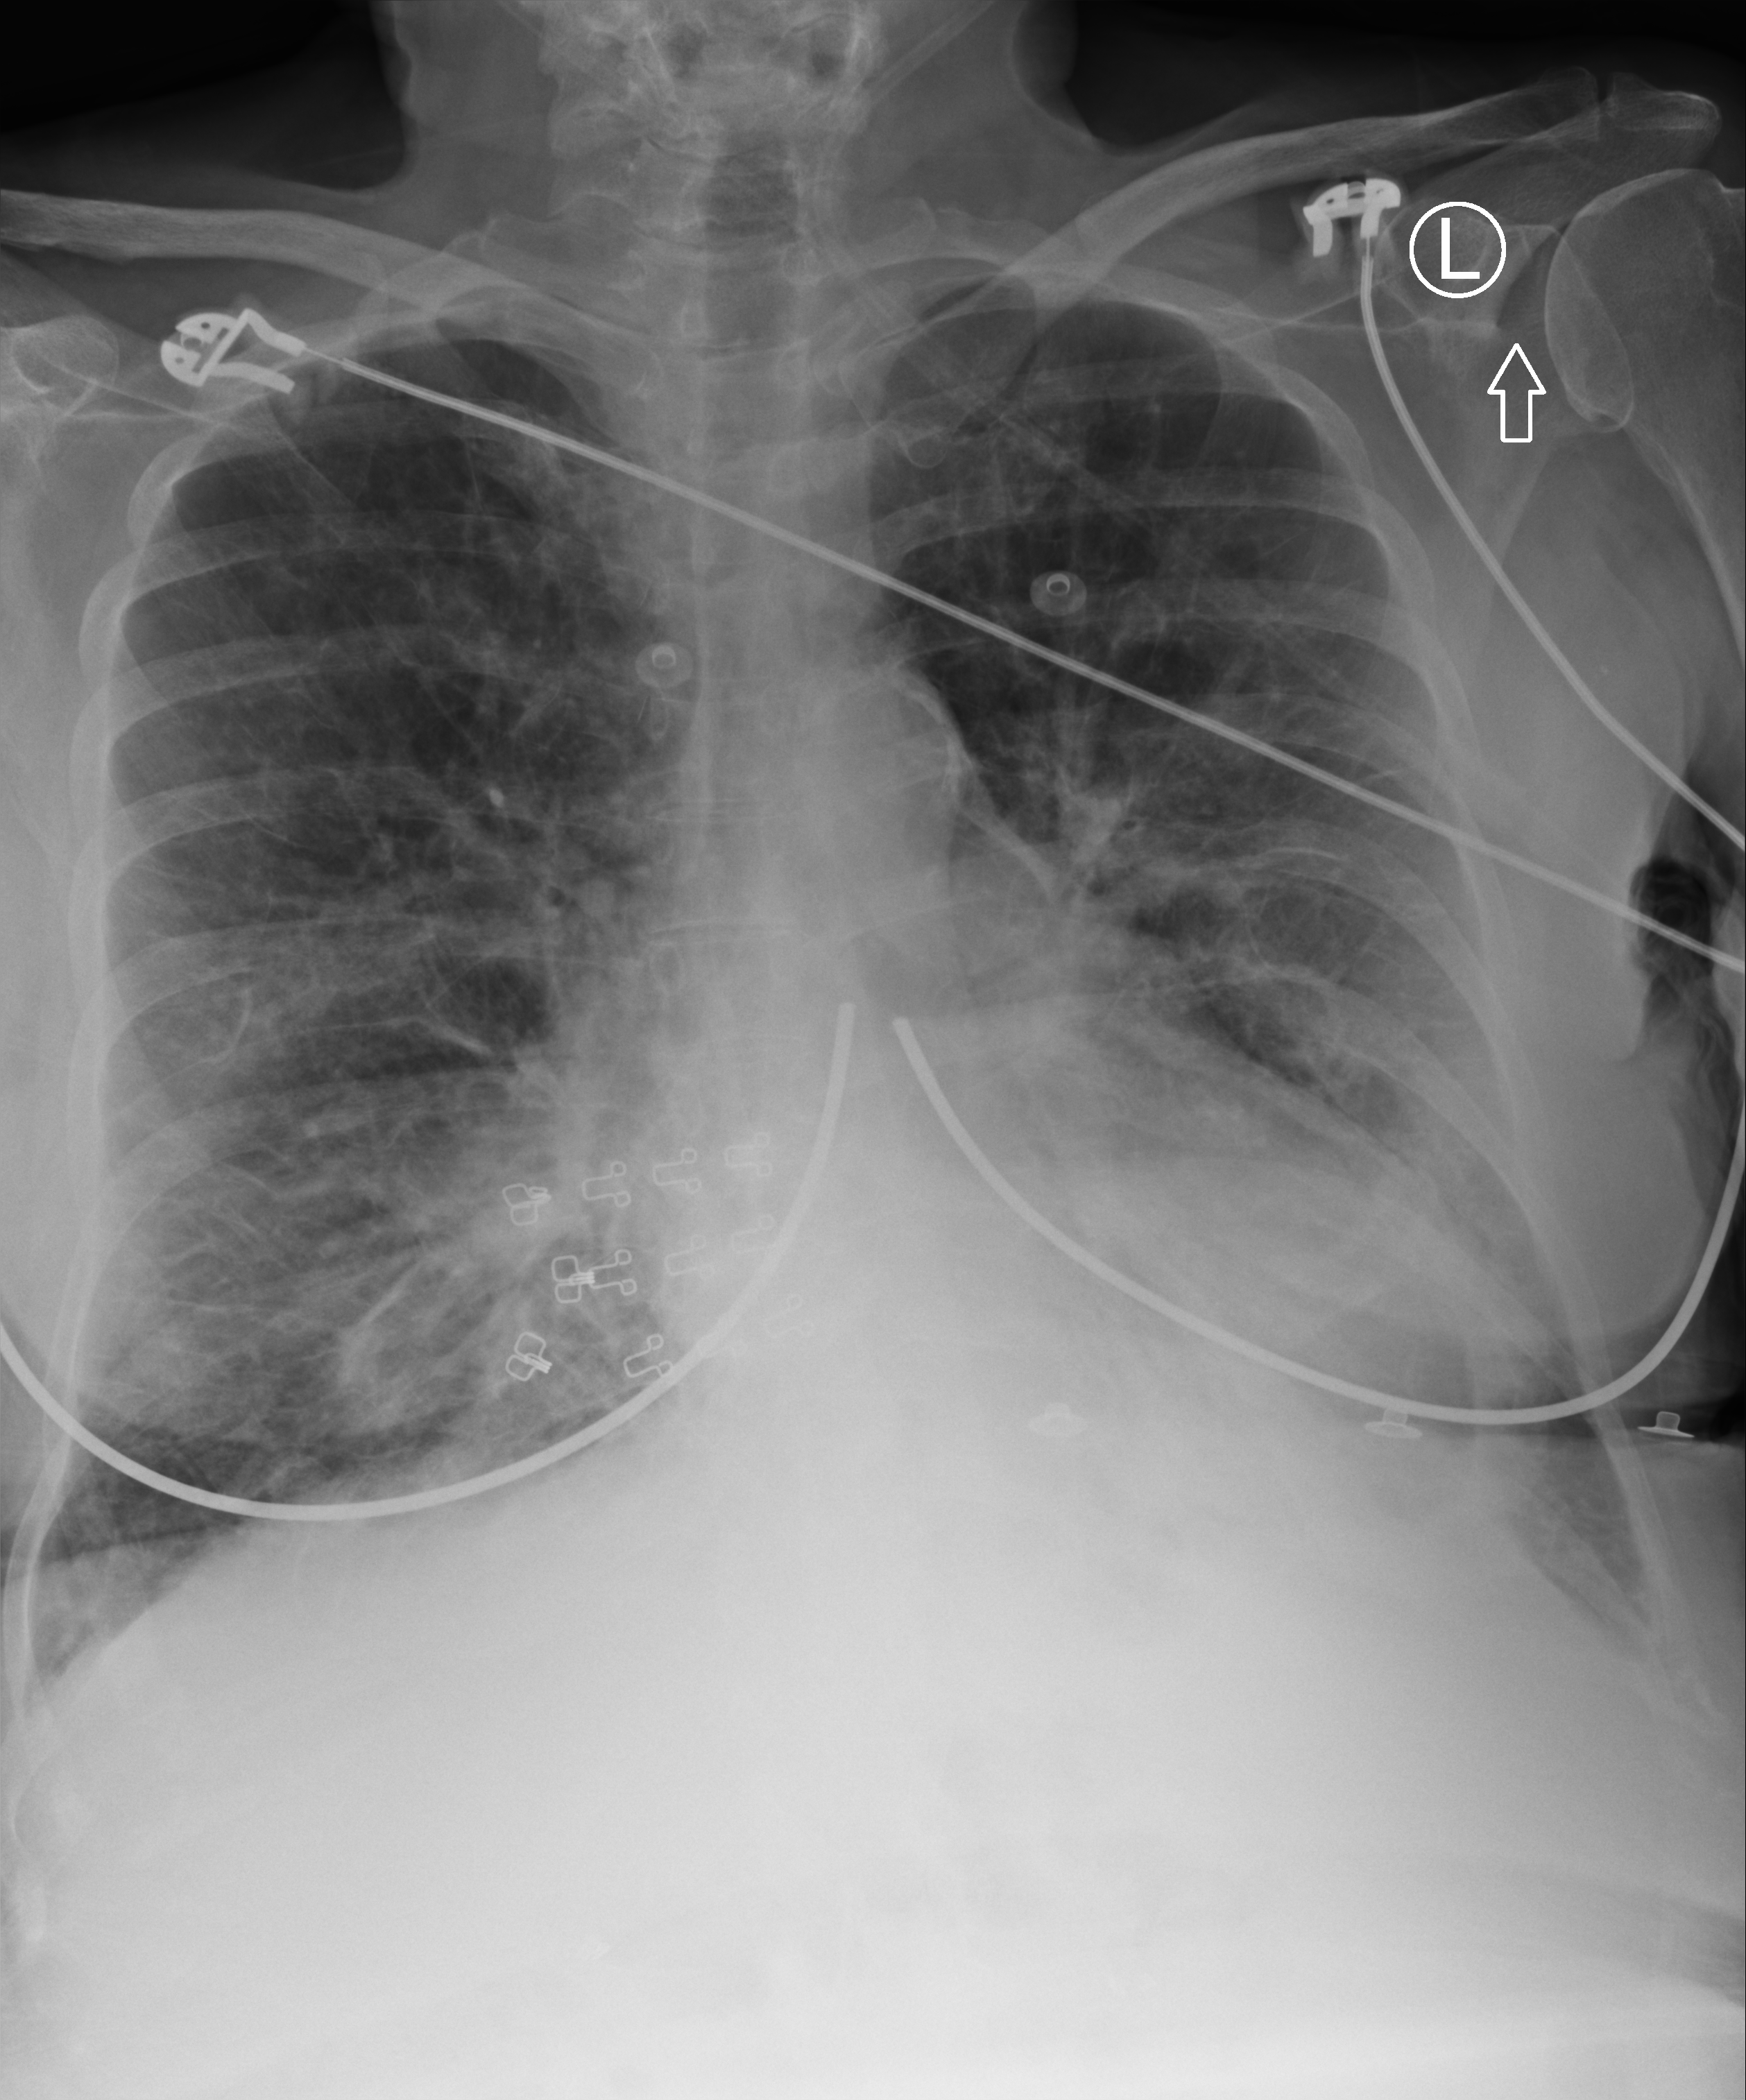
Portable chest radiograph; anteroposterior (AP) projection. Female patient hospitalised with COVID-19, age 18–59 years.
Admission-level facts for this patient (not findings on this image; timing relative to this image not recorded):
- mechanically ventilated during this hospital stay: no
- length of hospital stay: 11 days
- admitted to intensive care during this hospital stay: no